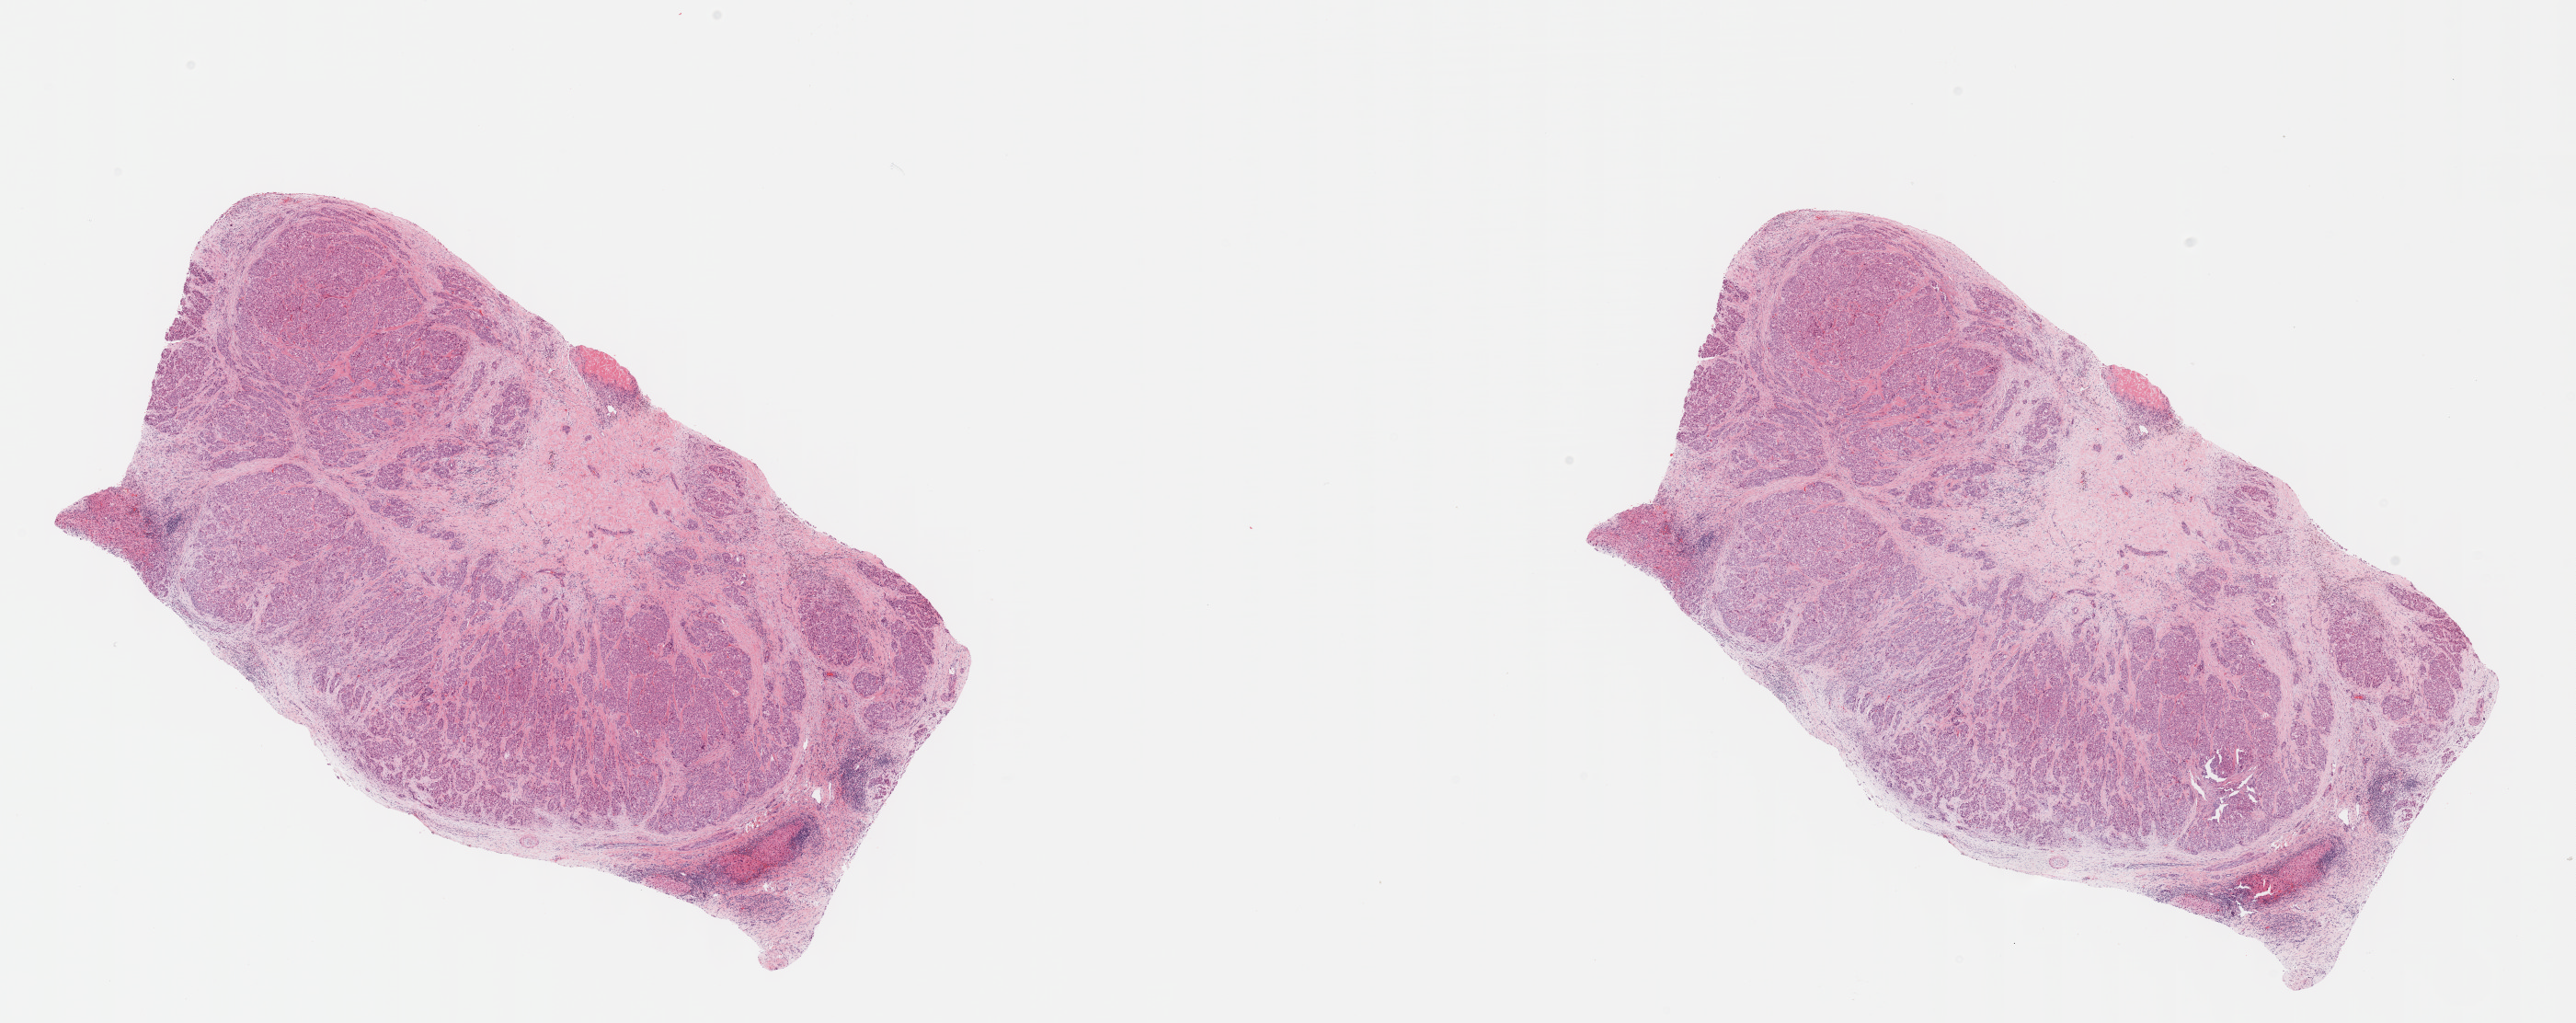
Whole-slide histology image, Hematoxylin and eosin (H&E) stained, shown as a low-resolution overview of the whole scanned area (about 22.6 x 9.0 mm, slide scanned at 40x); formalin-fixed paraffin-embedded (FFPE) diagnostic section; liver, primary tumour sample. Patient: male, age at initial diagnosis 48 years. Histologic grade: G3 (poorly differentiated).
- diagnosis: Hepatocellular carcinoma, NOS
- AJCC pathologic stage: II (6th edition)